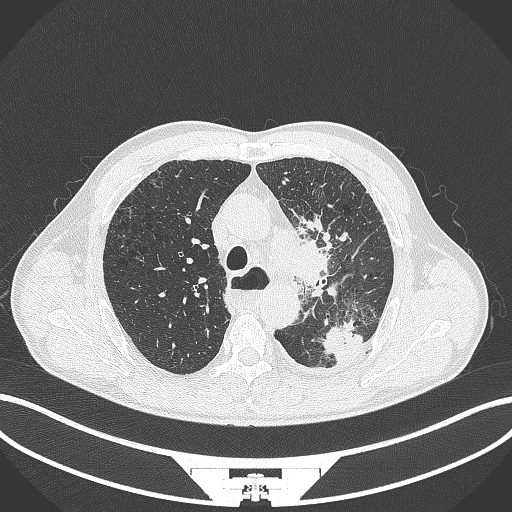
Chest CT, one axial slice; position 279 of 411 along the scan axis; reconstruction kernel B70f; lung window (W 1500 / L -600 HU); 1 mm slice thickness; 512 × 512 image matrix, field of view 400 × 400 mm. Patient: male, 57 years. From the clinical record (not read from this slice): clinical TNM (as recorded): T2a N1 M0.
Structures marked on this image (bounding box drawn by a radiologist):
- lung tumour (recorded histology: squamous cell carcinoma): box from (x=293, y=236) to (x=333, y=293) px